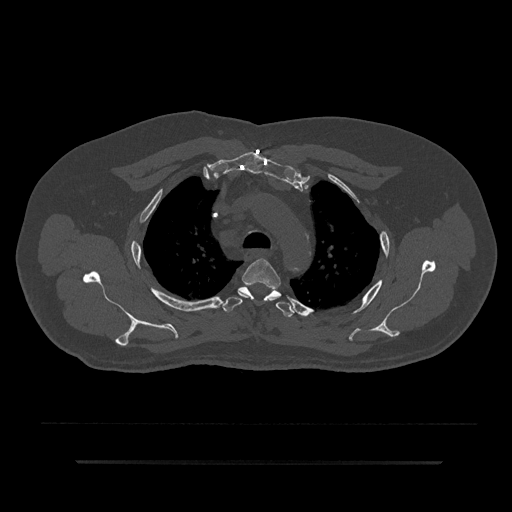
CT including the spine, one axial slice; position 640 of 797 along the scan axis; reconstruction kernel Br40s/3; bone window (W 1800 / L 400 HU); 0.5 mm slice thickness; 512 × 512 image matrix, field of view 464 × 464 mm. Male patient, age 59 years. From the clinical record (not read from this slice): primary cancer: bile ducts; vertebrae with lytic lesions (as recorded): T10.
Annotated regions visible in this slice (semi-automatically segmented with operator editing):
- T3 vertebra: bounding box [x1, y1, x2, y2] px = [239, 258, 281, 298]
- T4 vertebra: [222, 285, 294, 317]